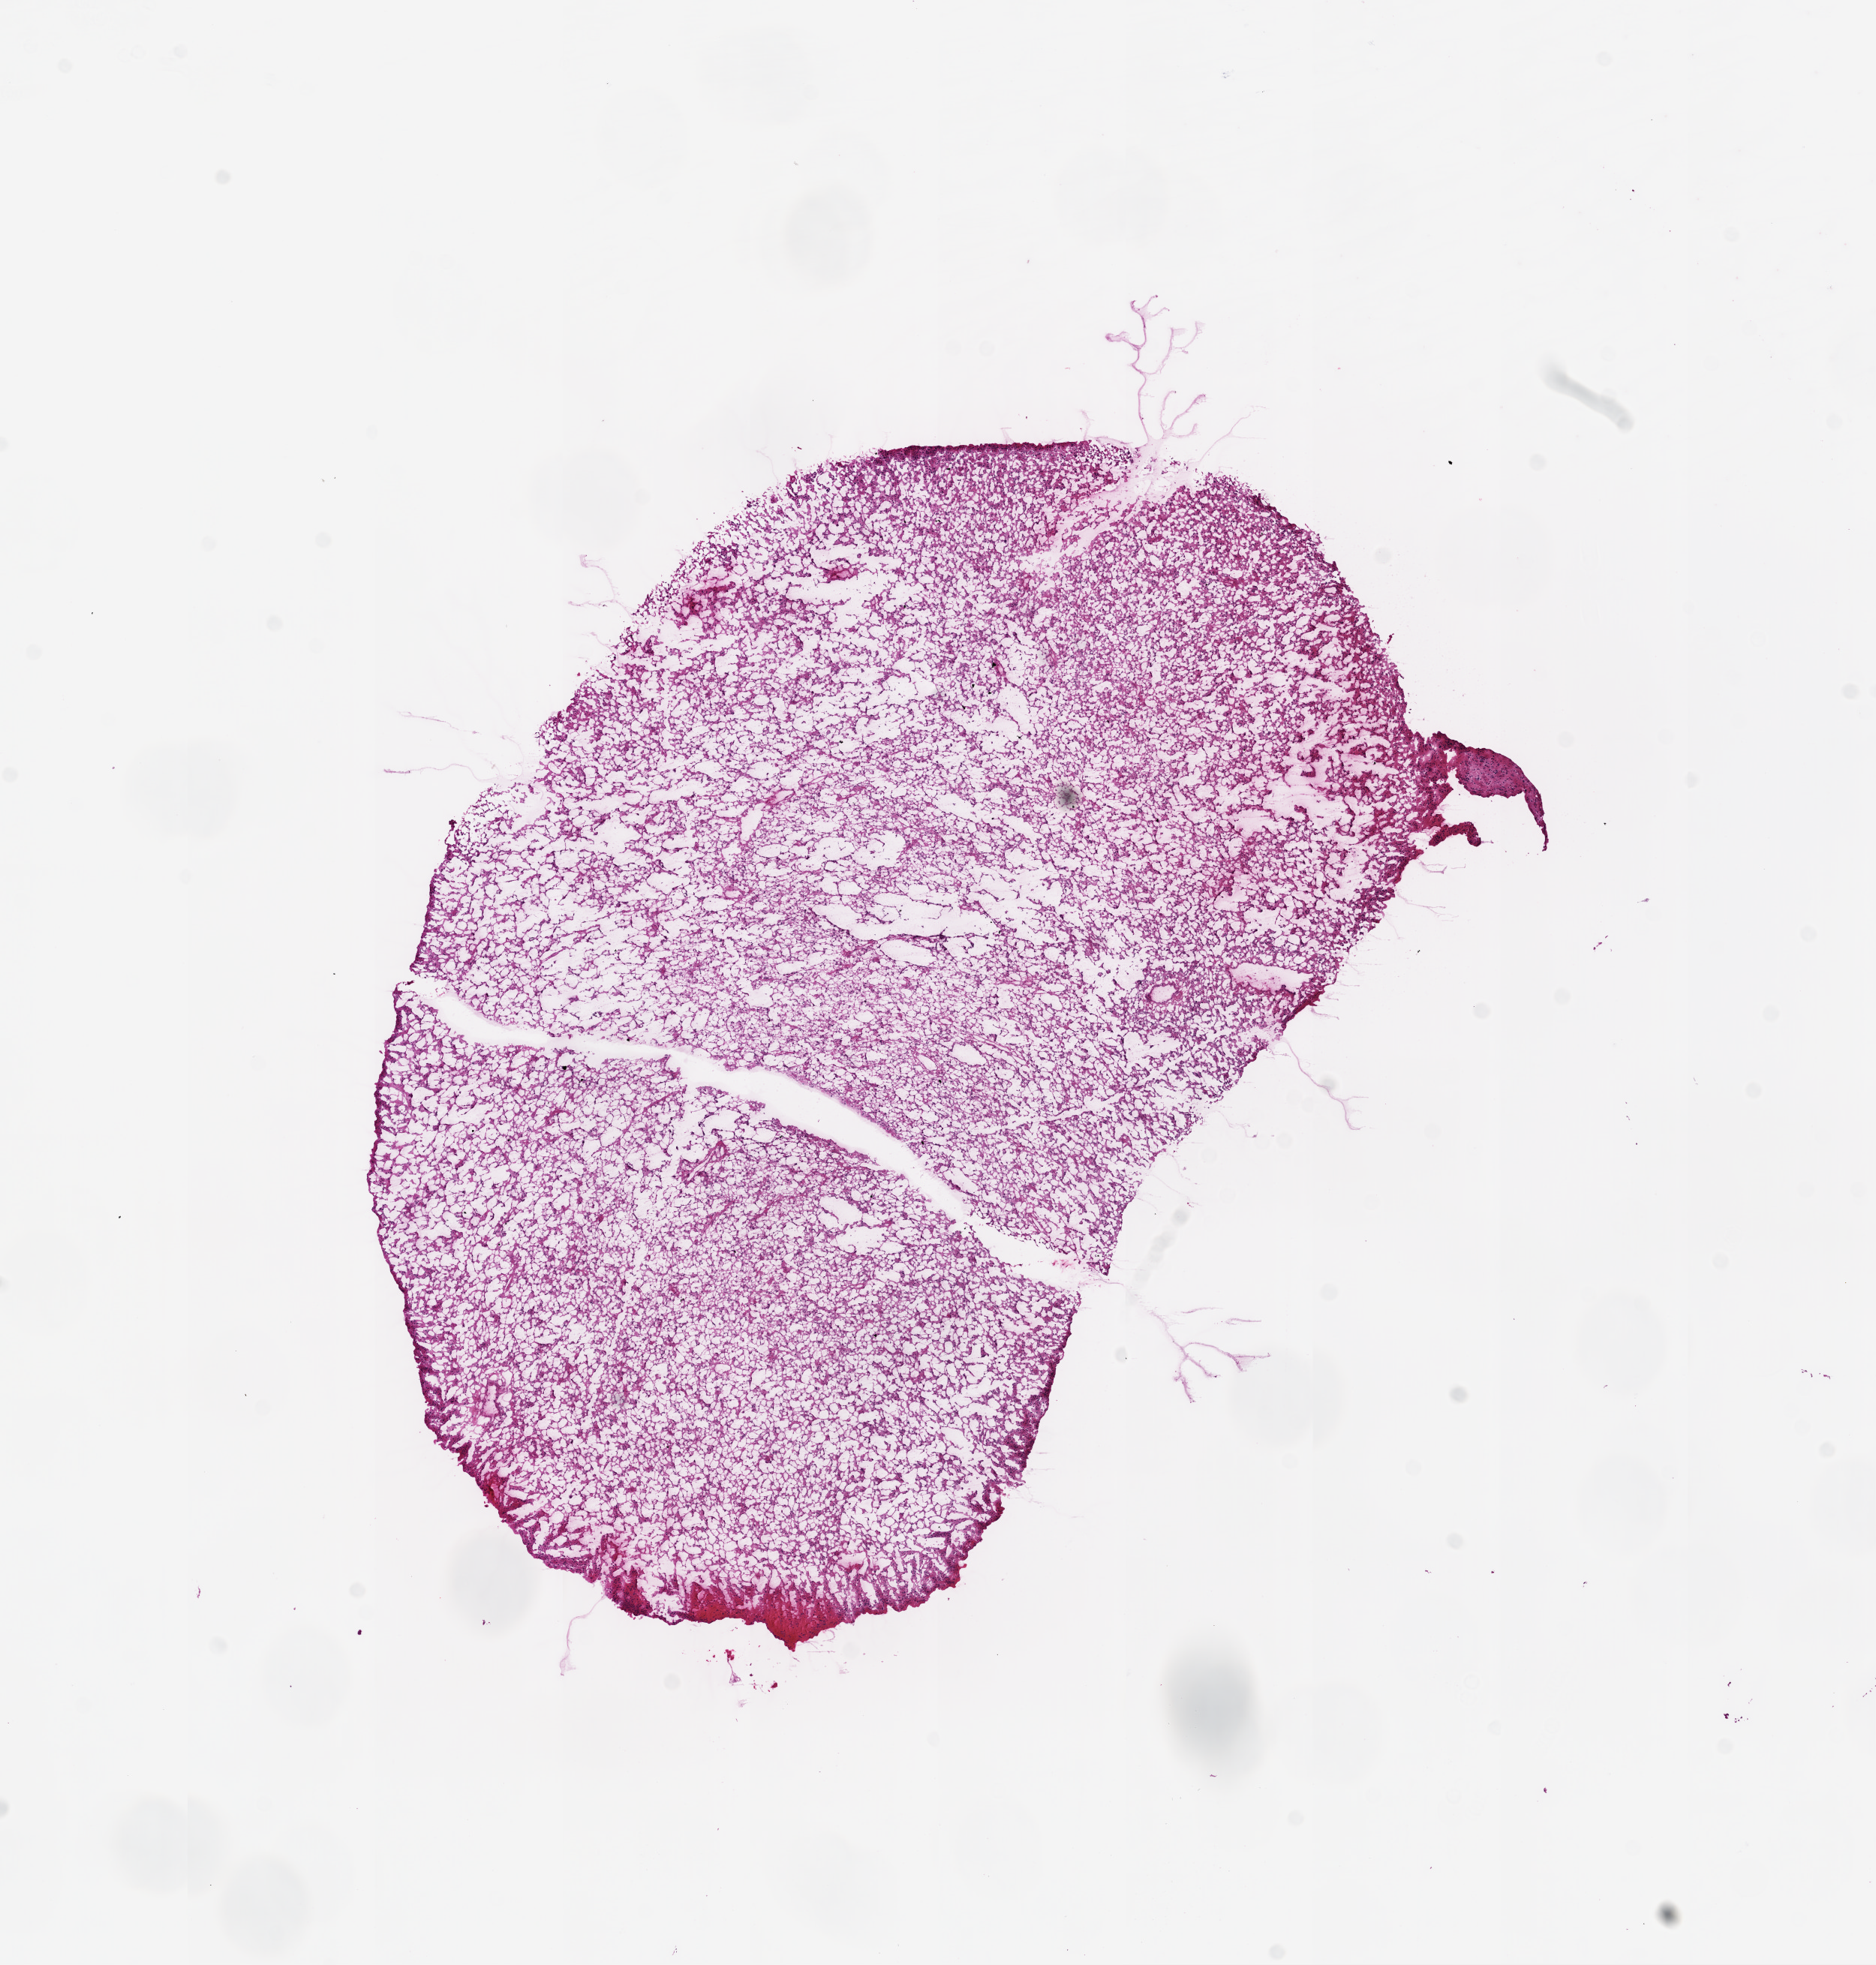
Digitized Hematoxylin and eosin (H&E) stained tissue section (whole slide), low-resolution overview of the scanned area, about 10.0 x 10.5 mm; frozen section from the top of the tissue portion; sample: primary tumour, brain. Female patient; age at initial diagnosis 38 years. Composition of this section per pathologist review: tumour cells 100%, tumour nuclei 75%.
Diagnosis: Mixed glioma.